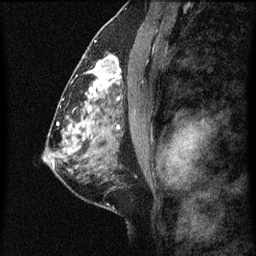
Breast MRI (dynamic contrast-enhanced), one sagittal slice; slice 36 of 60 in the series (ordered by position); dynamic contrast-enhanced series, image 2 of 7 at this slice position (ordered by acquisition); 1.5 T; TE 4.2 ms, TR 8 ms; 256 × 256 image matrix. Female patient, age 51 years.
Annotated regions visible in this slice (semi-automatic segmentation, software-assisted and operator-edited):
- analysis volume of interest (the breast-tissue region the enhancement analysis was run in; not a lesion): bounding box <86,48,125,101> (left, top, right, bottom; pixels)
- tumour enhancement mask (voxels above the 70 % enhancement threshold inside the analysis volume of interest): <86,58,122,101>